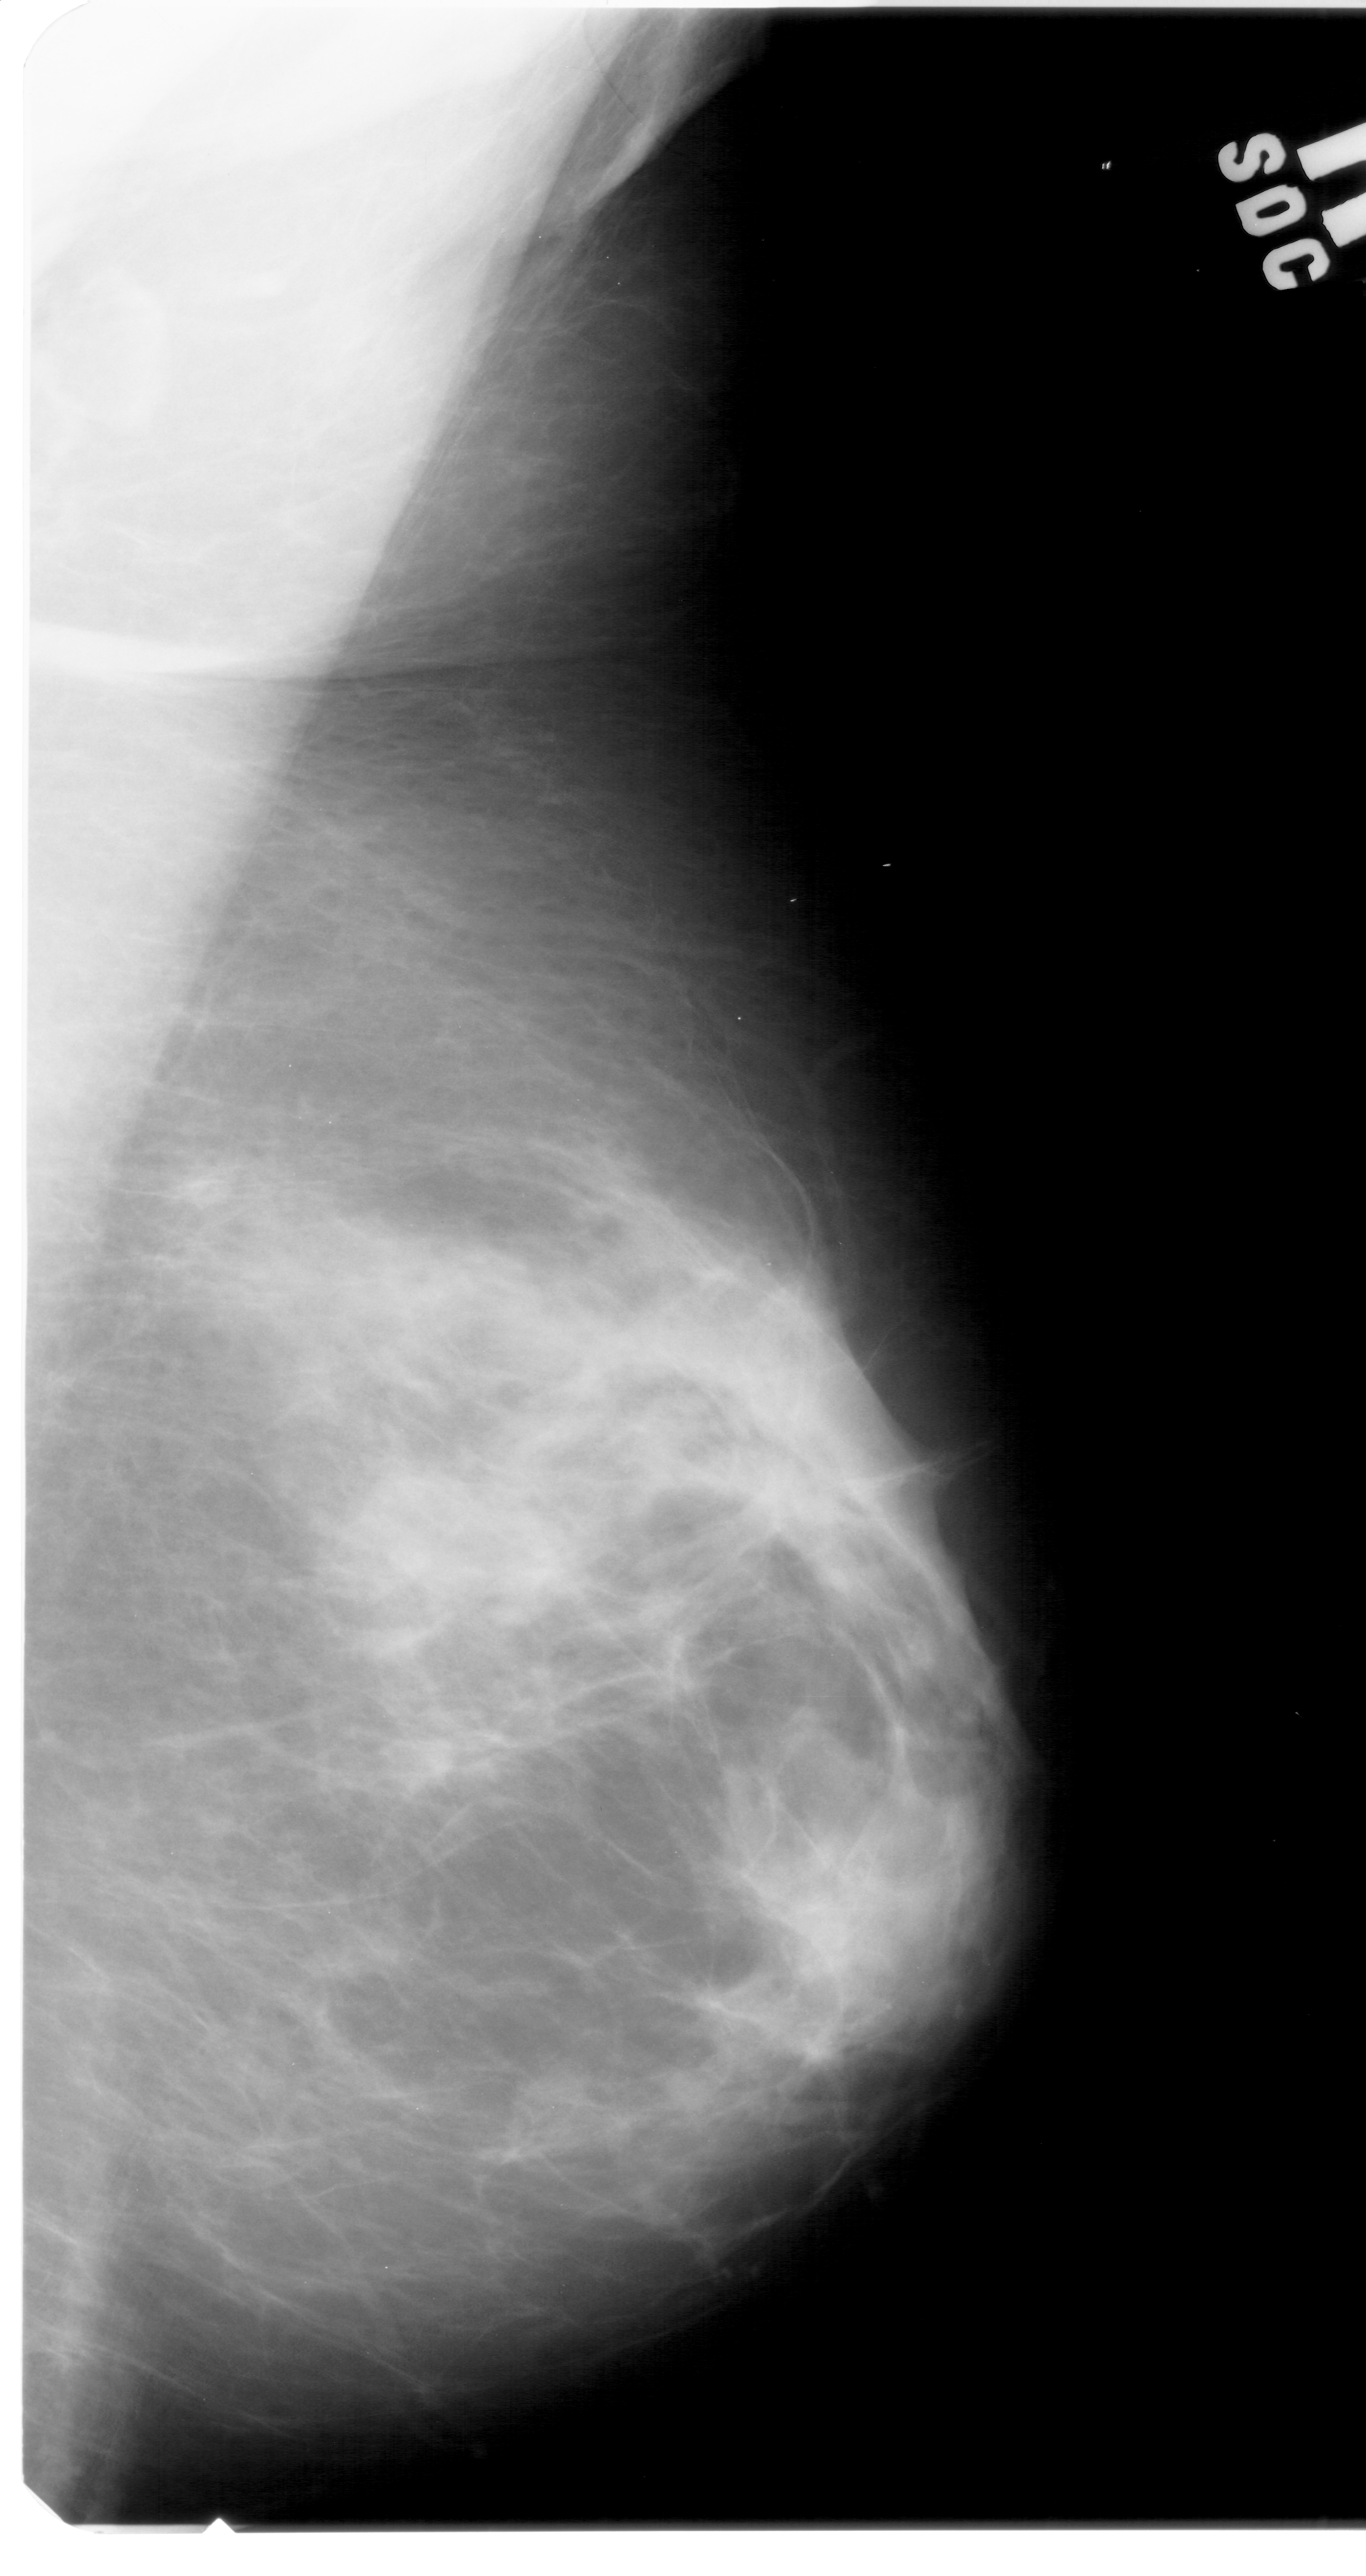
Scanned film-screen mammogram; right breast; mediolateral oblique (MLO) view; breast composition: extremely dense (BI-RADS density category 4 of 4).
- Abnormality record for this image: mass, shape irregular, margins spiculated; BI-RADS assessment category 5; pathology (as recorded): malignant.